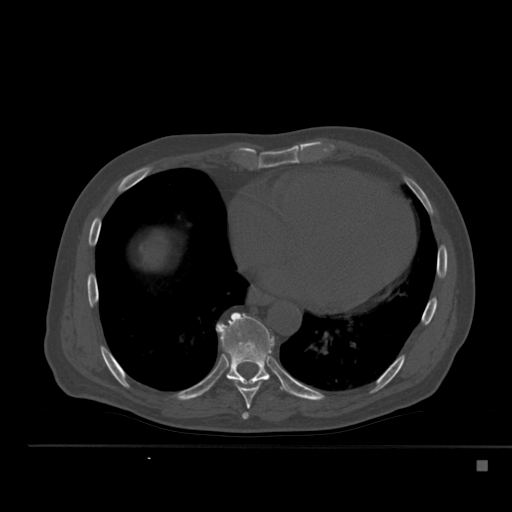
CT including the spine, one axial slice. Position 298 of 517 along the scan axis. 120 kVp. Bone window (W 1800 / L 400 HU). 1.5 mm slice thickness. 512 × 512 image matrix, field of view 408 × 408 mm. Male patient, age 70 years. Case-level facts recorded for this patient, not image findings: primary cancer: renal.
Outlined on this slice (semi-automatic segmentation, software-assisted and operator-edited):
- T7 vertebra: box from (x=242, y=412) to (x=249, y=420) px
- T8 vertebra: (x=231, y=379)–(x=269, y=409)
- T9 vertebra: (x=216, y=312)–(x=281, y=389)